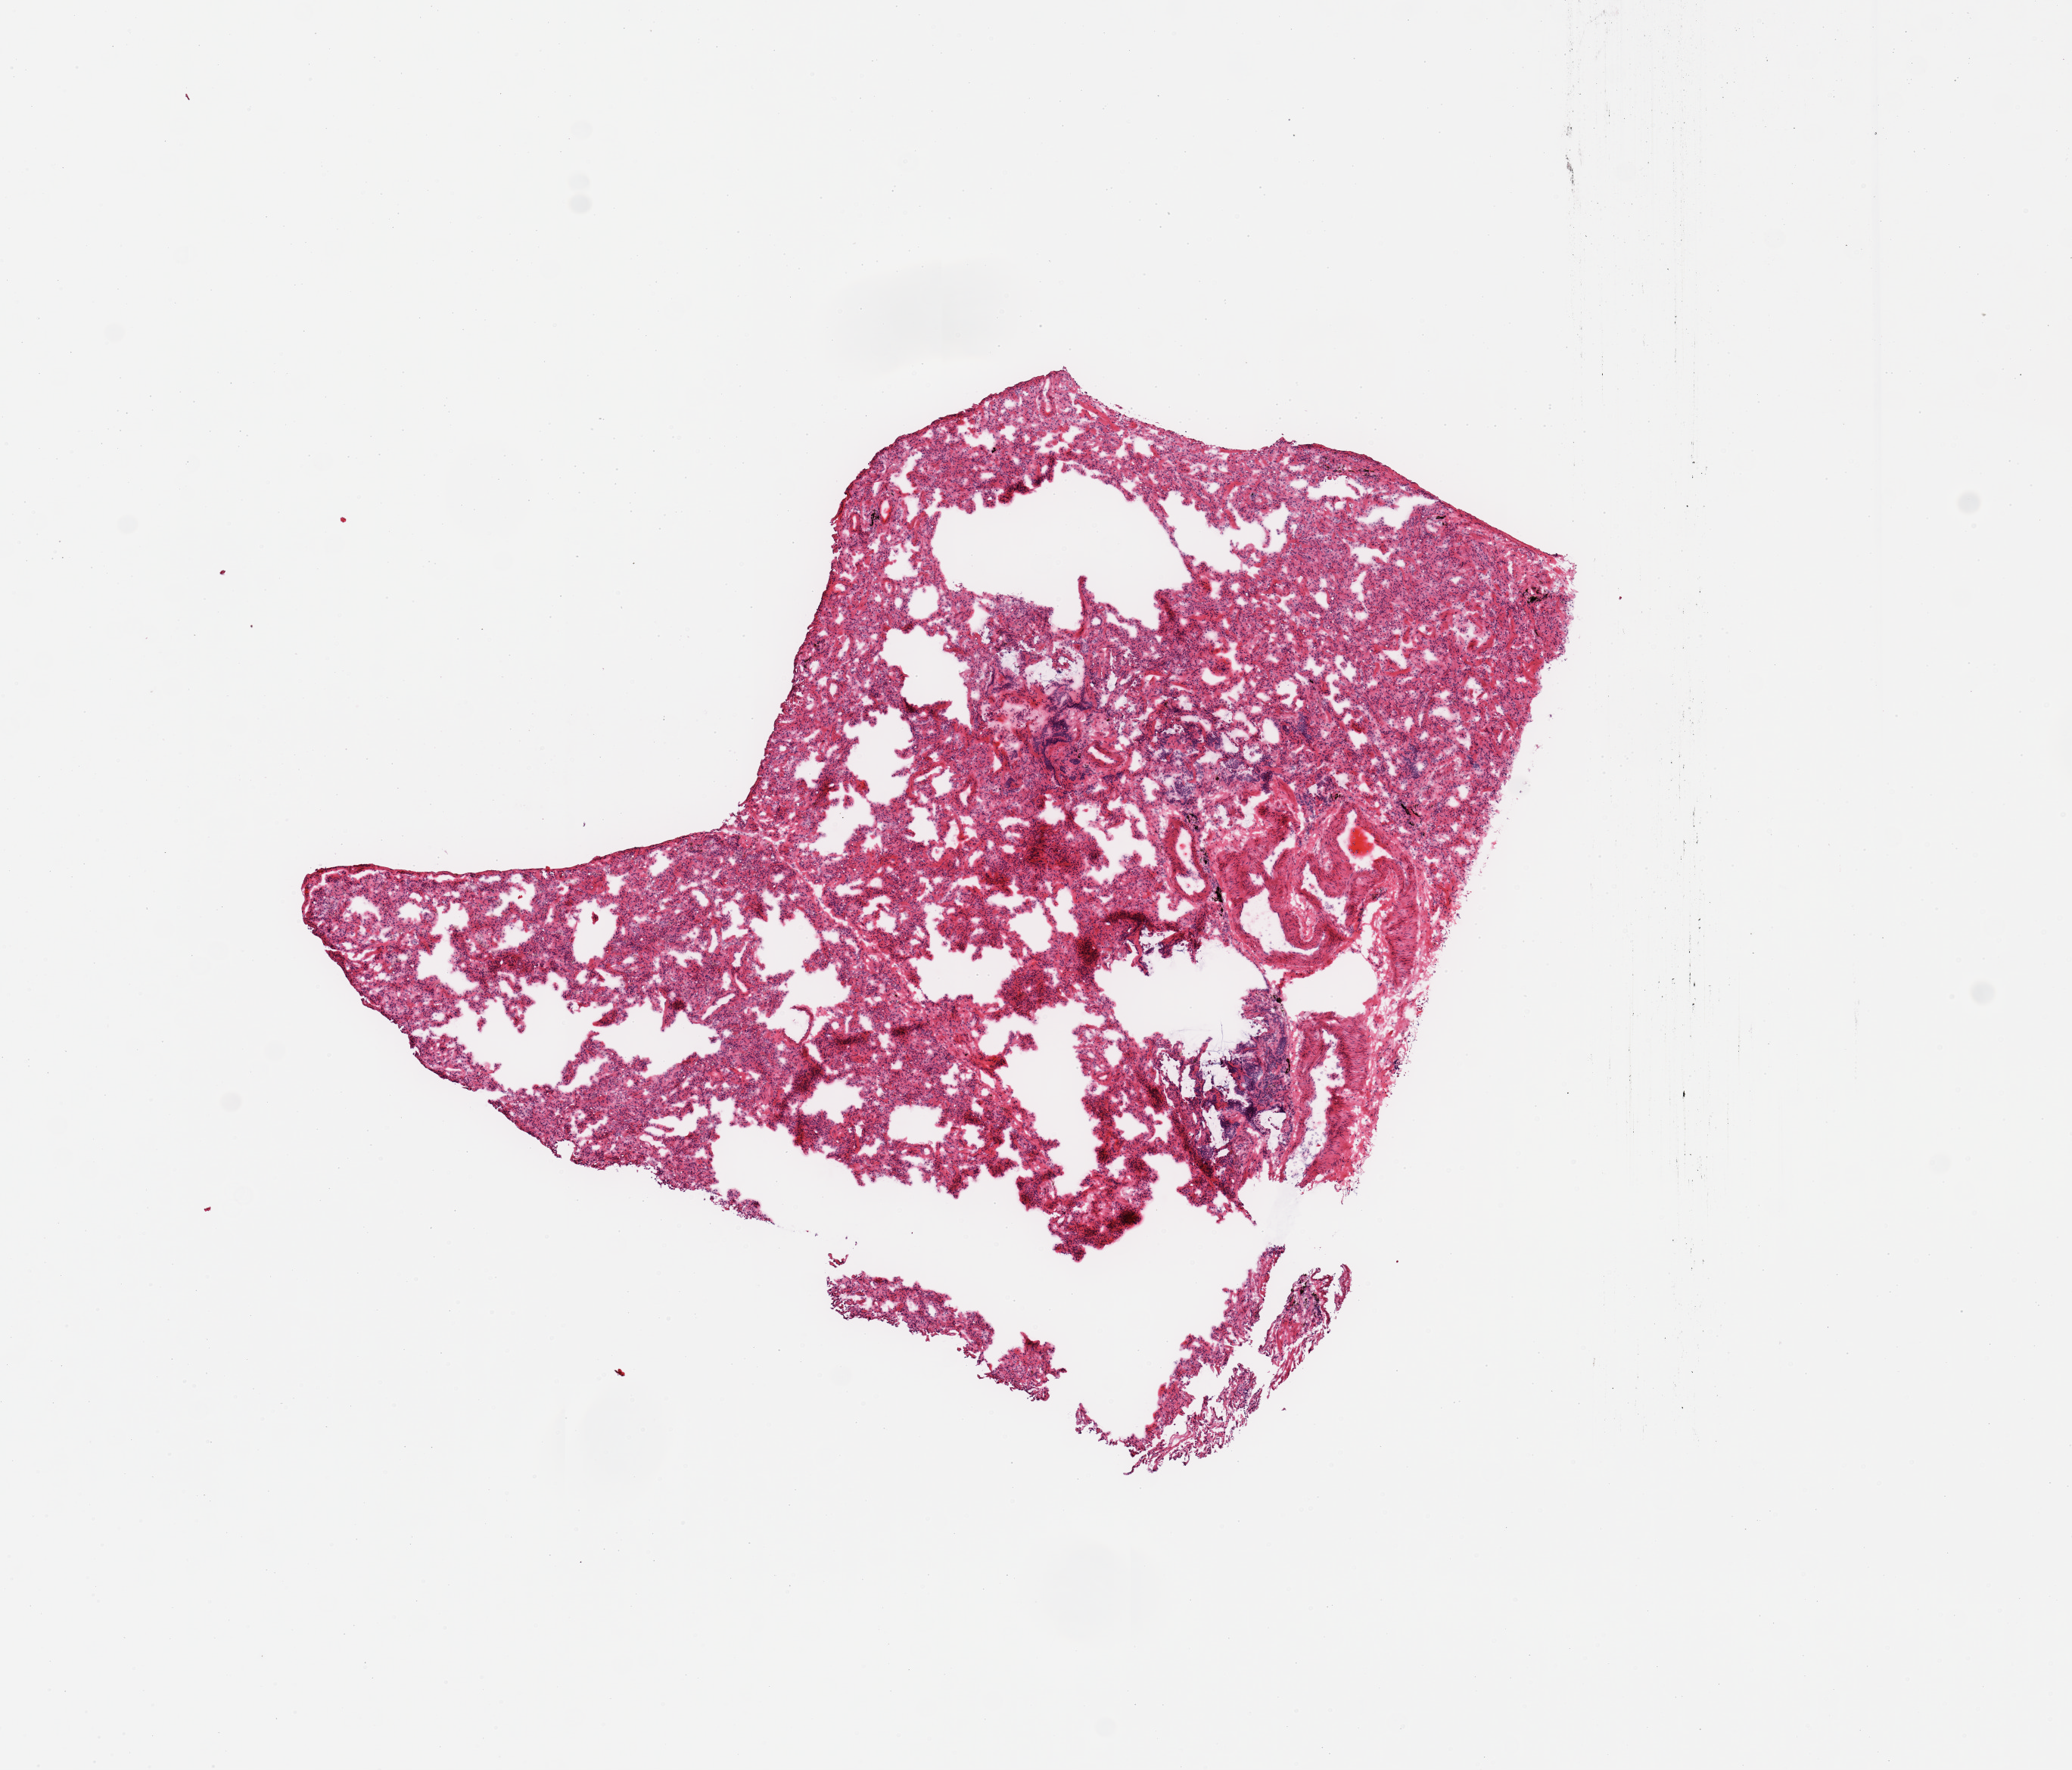
Whole-slide image, hematoxylin and eosin (H&E) stain, low-resolution overview of the scanned area, about 10.8 x 9.3 mm. Donor sex: male.
* specimen: frozen section (dry ice); target tissue: lung; donor tissue sample